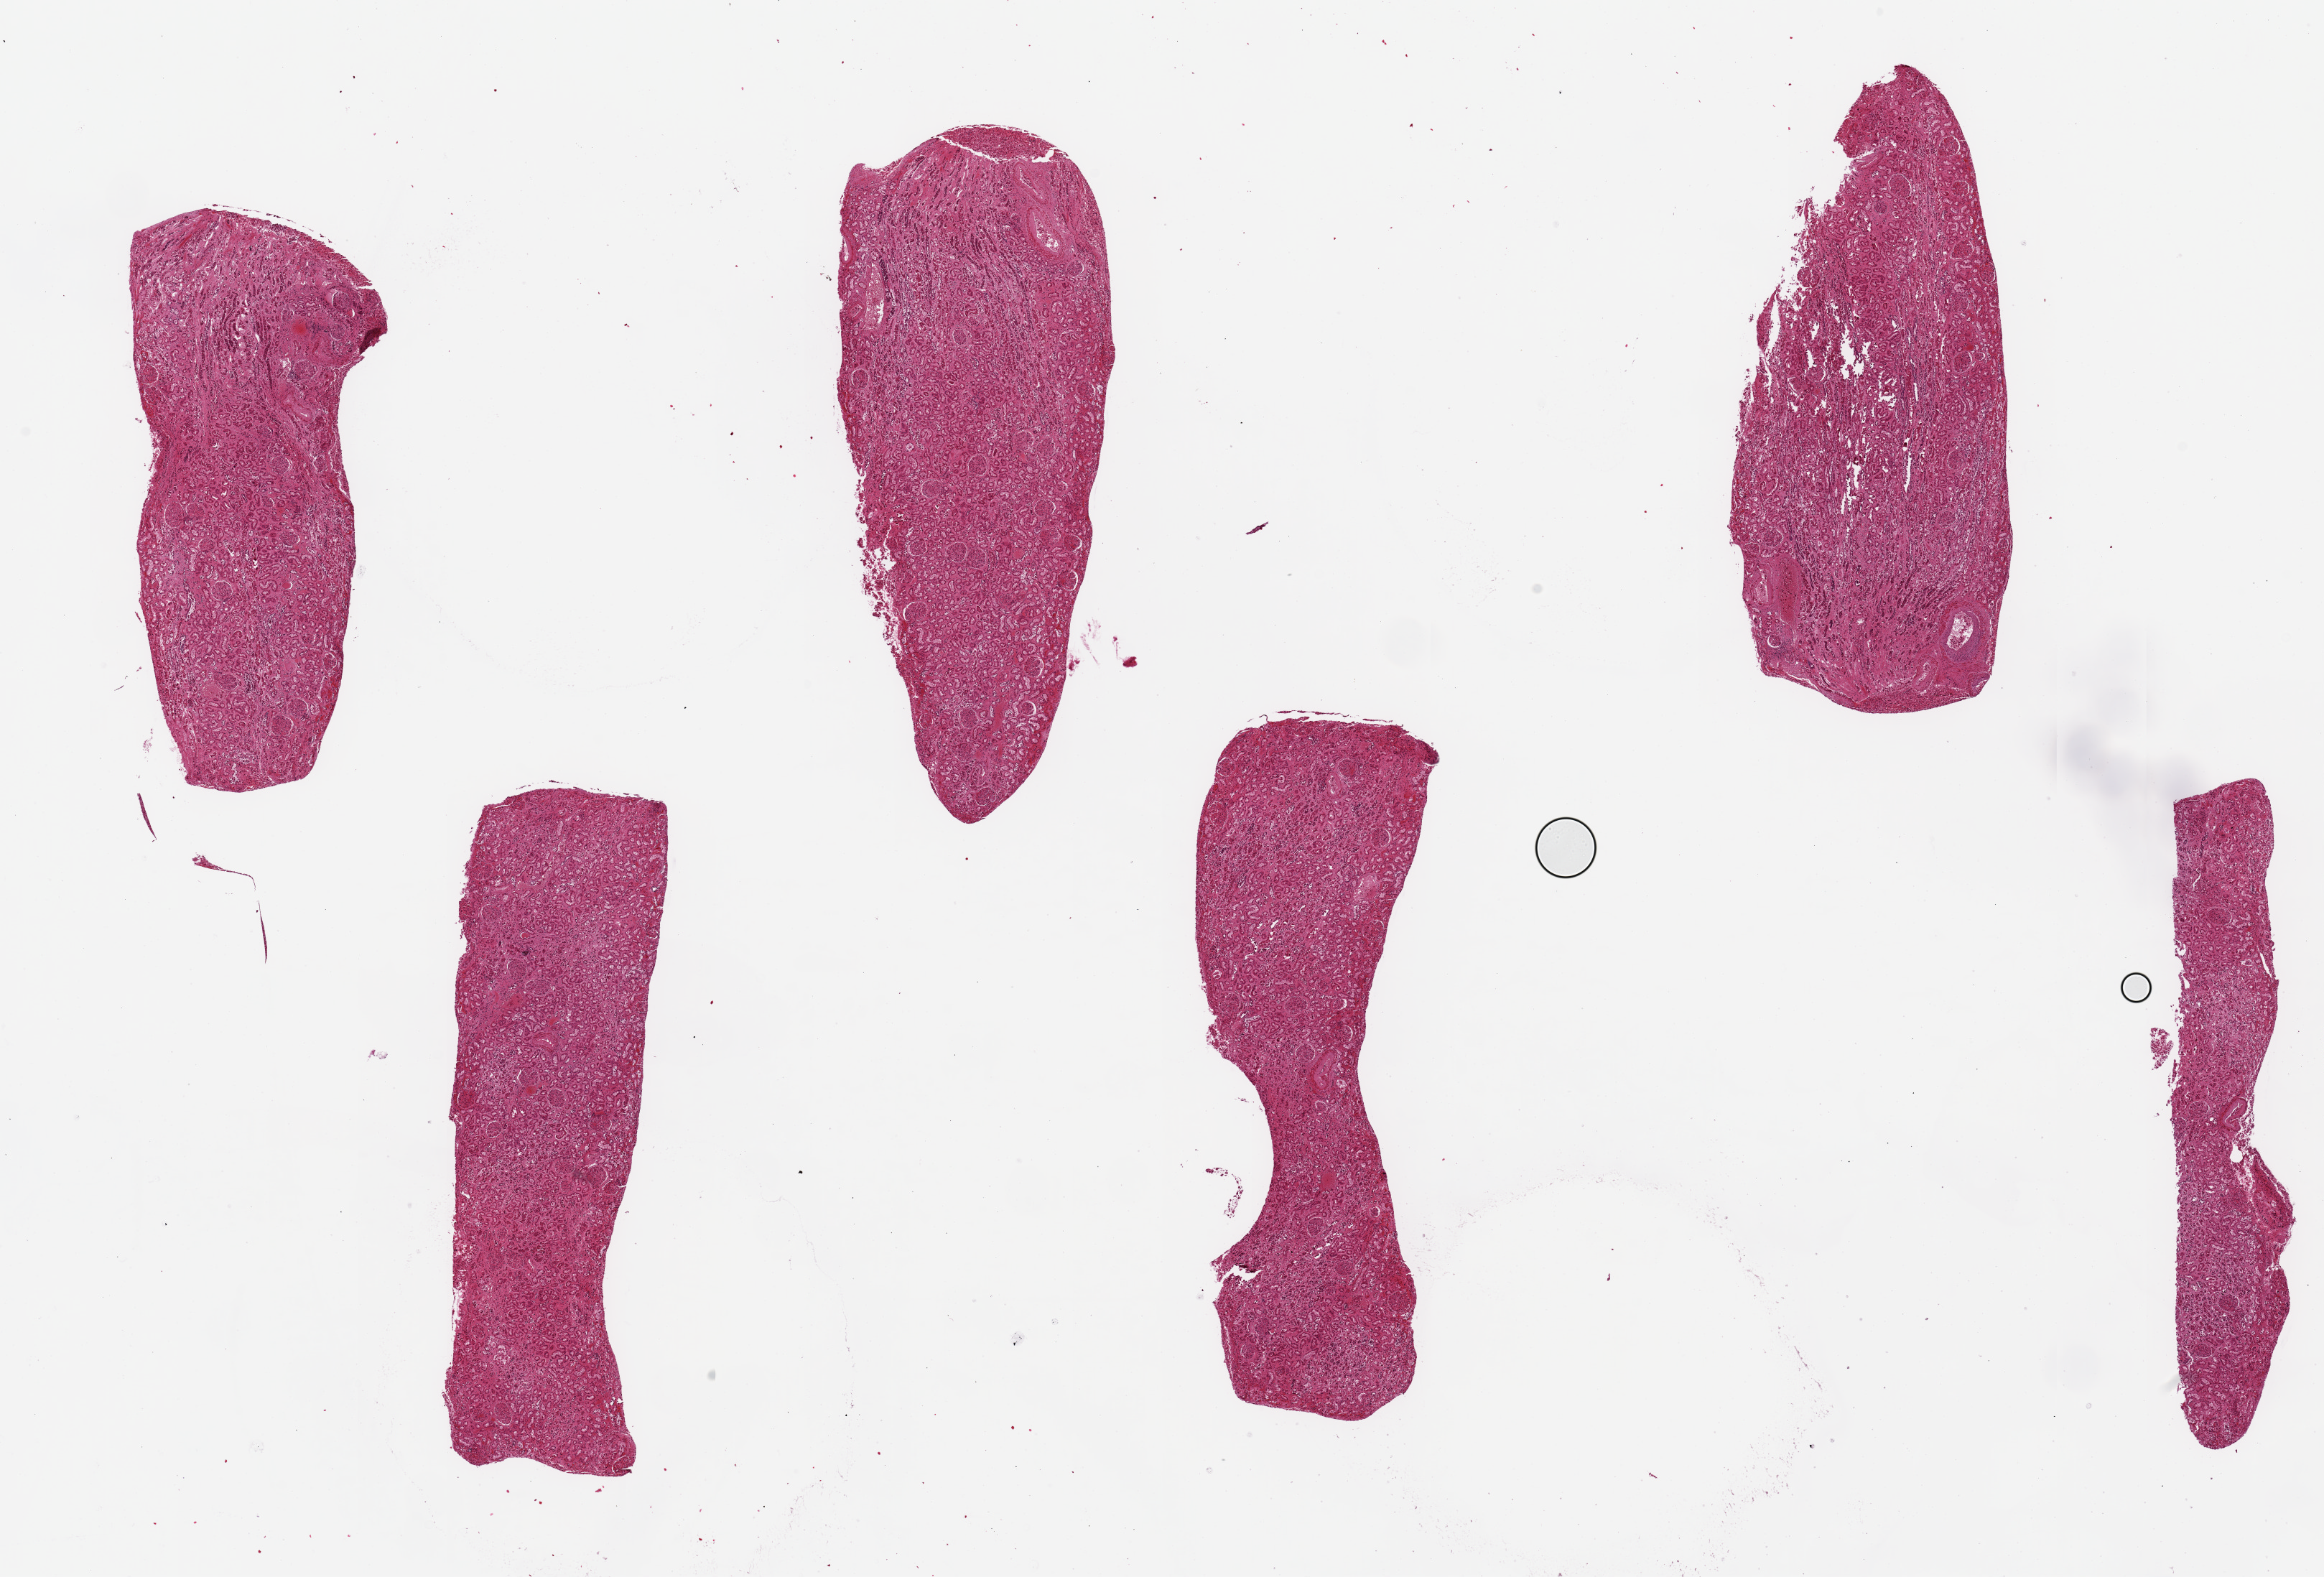
Digitized hematoxylin and eosin (H&E)-stained section, low-resolution overview of the scanned area, about 25.6 x 17.4 mm (slide scanned at 20x), PAXgene-fixed paraffin-embedded (PFPE) section, sampled site (target tissue): renal cortex, tissue donor sample. Donor sex: male.
Reviewer comment on this tissue sample: 6 pieces, up to 8x3mm.